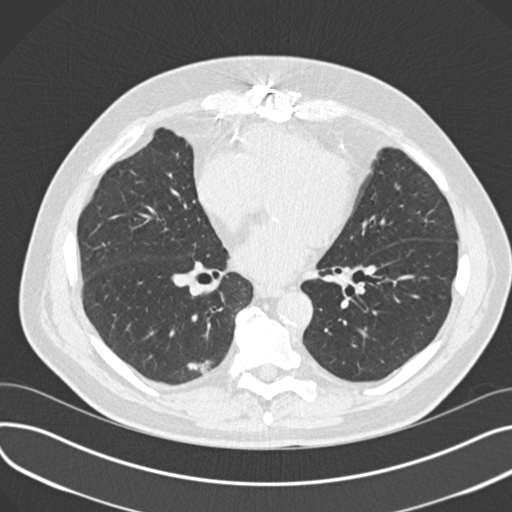
Low-dose screening chest CT, one axial slice. Slice 79 of 177 in the series (ordered by position). Reconstruction kernel B30f. 120 kVp. Lung window (W 1500 / L -600 HU). 2 mm slice thickness. 512 × 512 image matrix.
Structures marked on this image (manually delineated by an expert):
- lesion 1 (tumor, lower lobe of right lung): bounding box <187,360,212,376> (left, top, right, bottom; pixels)